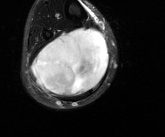
MRI of an extremity soft-tissue mass, one axial slice; position 51 of 81 along the scan axis; T2-weighted fat-saturated; MR volume resampled by the dataset authors to the PET/CT grid (not the native acquisition matrix); 3.27 mm slice thickness; 165 × 137 image matrix, field of view 161 × 134 mm. Male patient. From the clinical record (not read from this slice): histological type: liposarcoma - round cell; grade: high; site of the primary tumour: right calf.
Structures marked on this image (expert contour drawn on MRI and transferred to this co-registered scan by the dataset authors):
- gross tumour volume (mass): box from (x=32, y=27) to (x=108, y=97) px